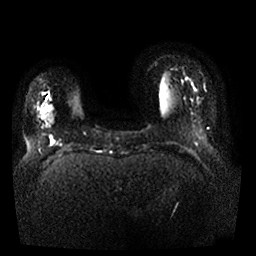
Breast MRI, one axial slice. Position 2 of 25 along the scan axis. Diffusion-weighted series; image 2 of 4 stored at this slice position (different b-values; order by instance number). 1.5 T. 4 mm slice thickness. 256 × 256 image matrix, field of view 350 × 350 mm. Female patient.
Annotated regions visible in this slice (manually delineated by an expert):
- tumour on diffusion-weighted imaging: box from (x=40, y=106) to (x=48, y=120) px